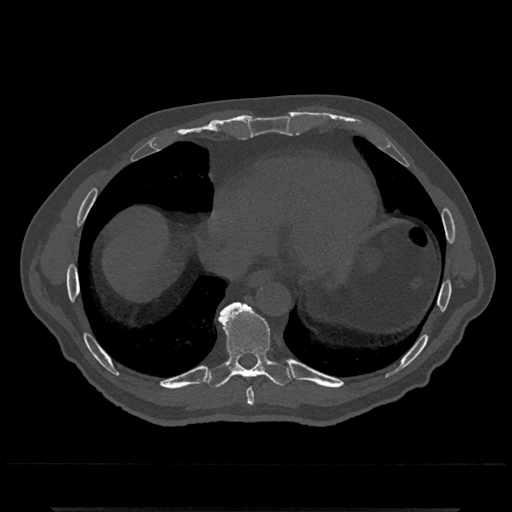
CT including the spine, one axial slice; slice 623 of 797 in the series (ordered by position); reconstruction kernel Br40s/3; 120 kVp; bone window (W 1800 / L 400 HU); 0.5 mm slice thickness; 512 × 512 image matrix. Male patient, age 67 years. From the clinical record (not read from this slice): primary cancer: prostate.
Outlined on this slice (semi-automatic segmentation, software-assisted and operator-edited):
- T8 vertebra: bounding box <246,388,255,406> (left, top, right, bottom; pixels)
- T9 vertebra: <204,302,294,389>